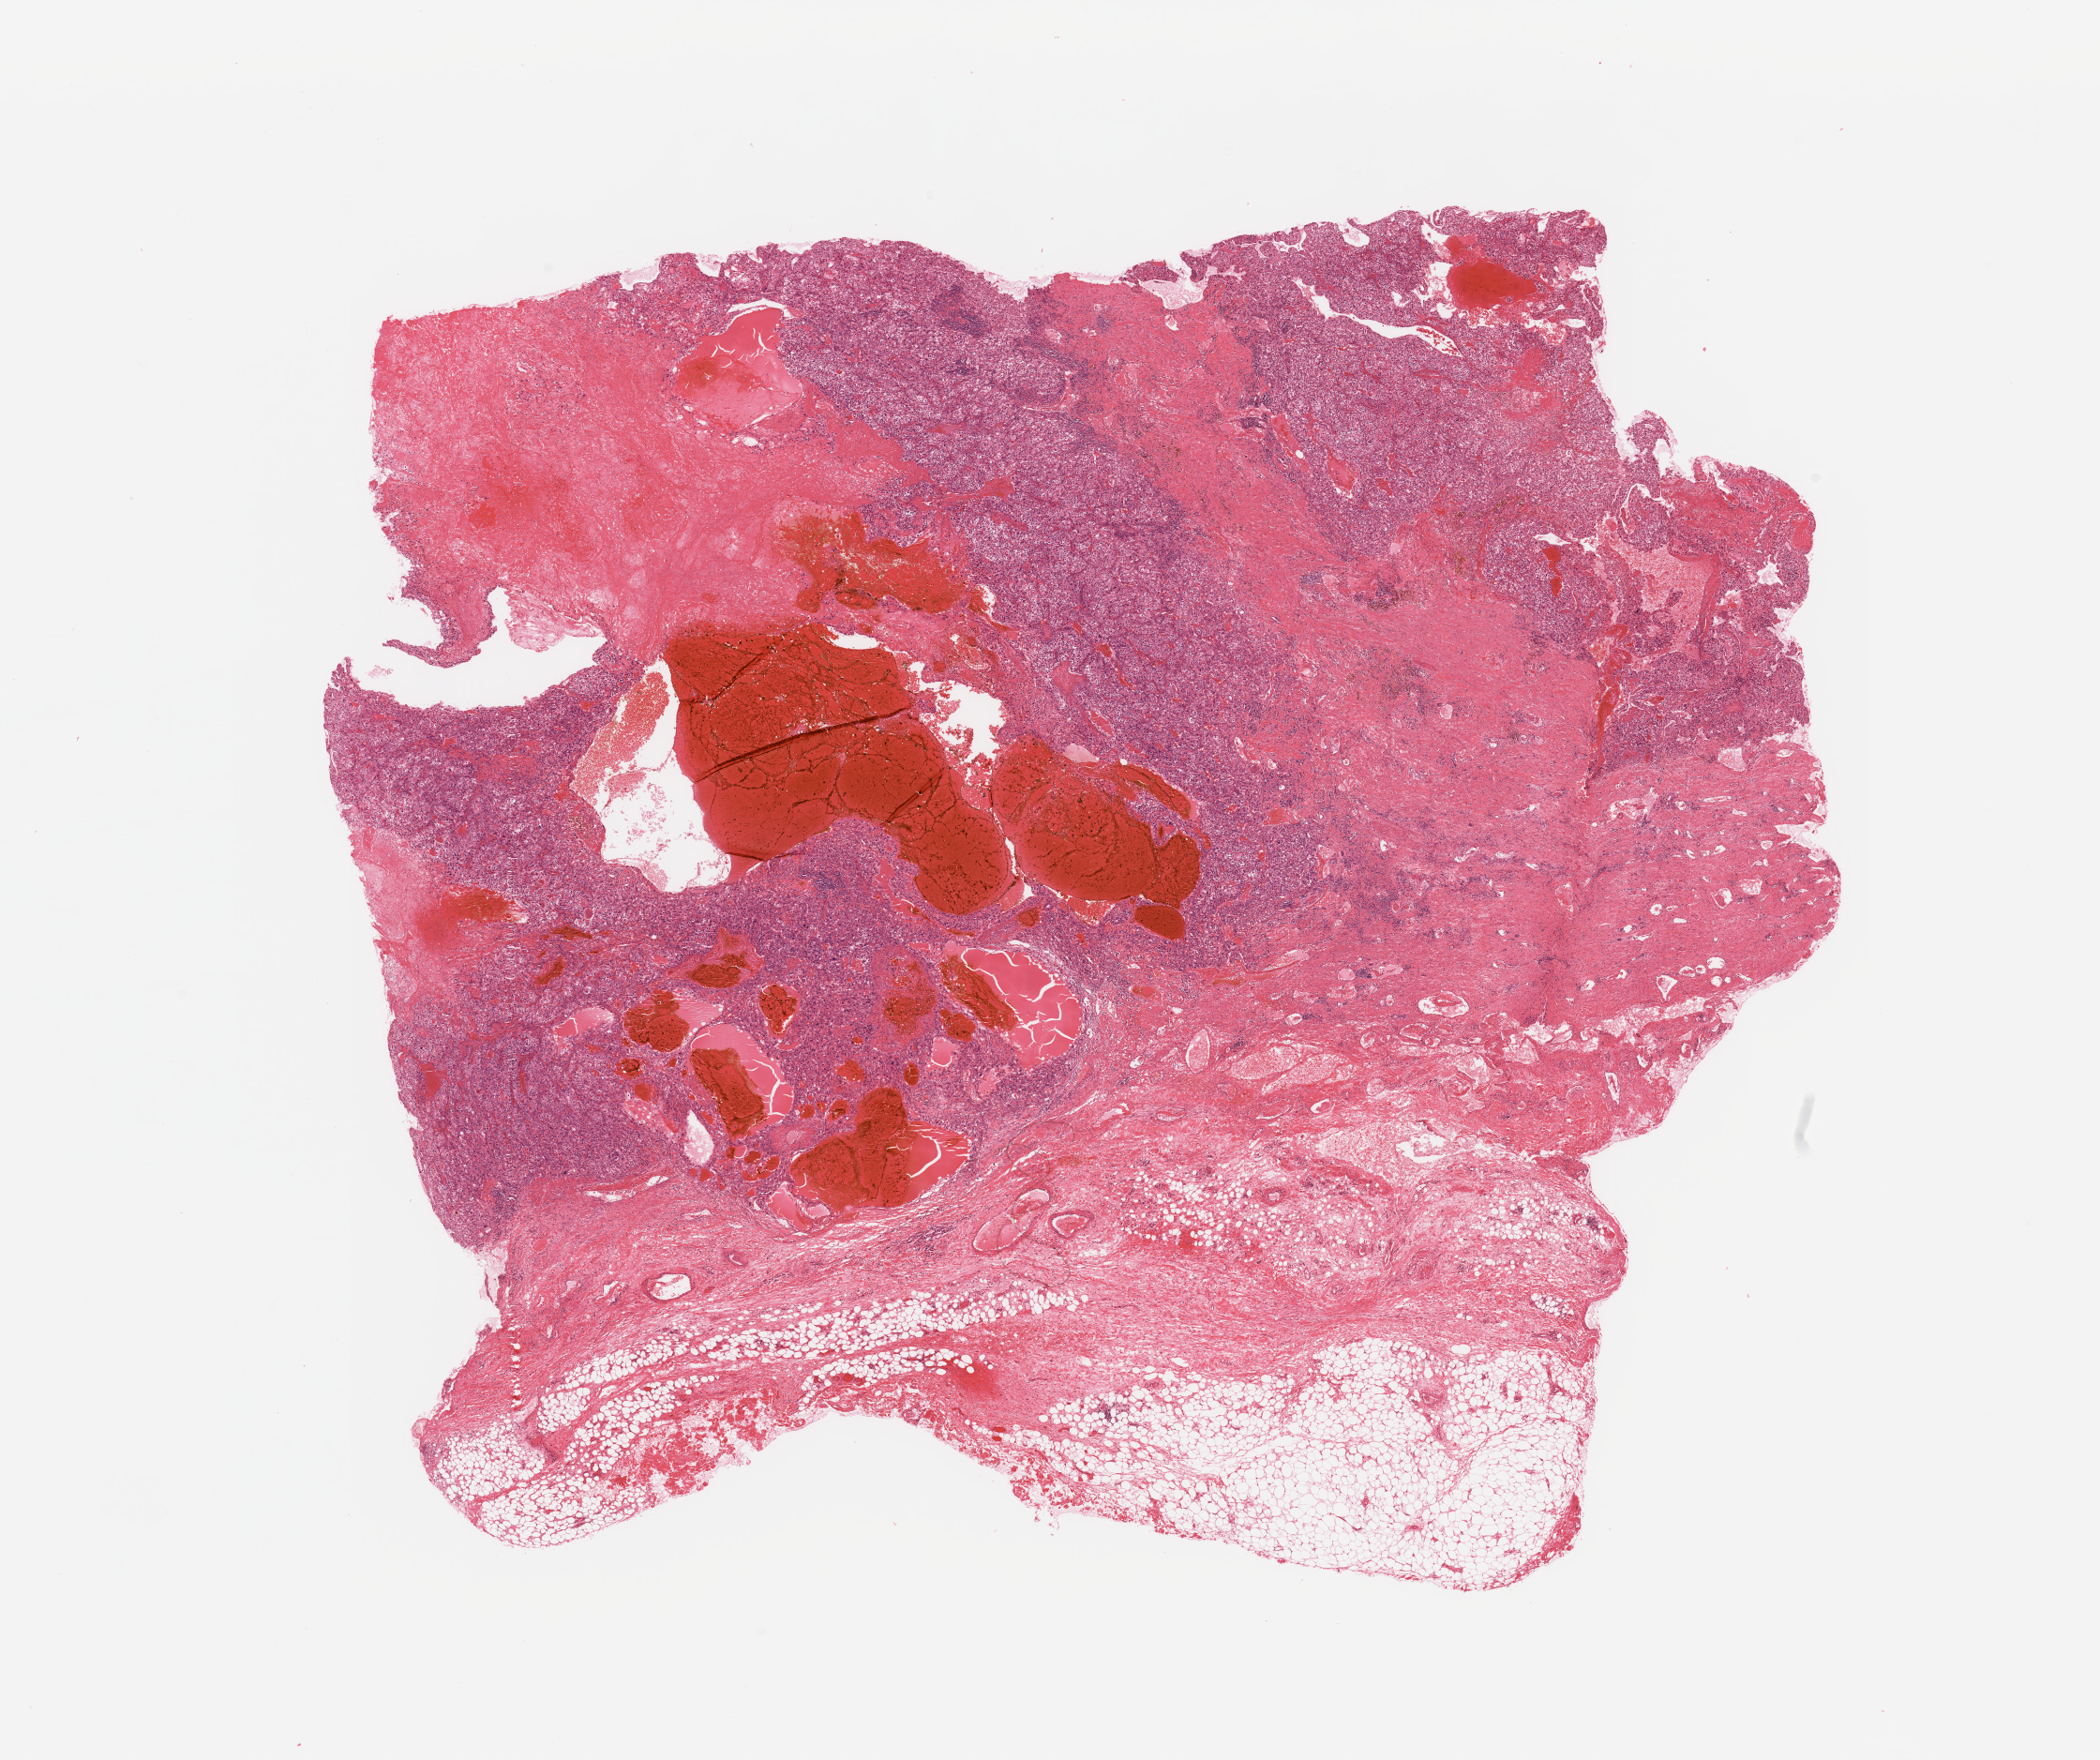
Whole-slide histology image, H&E — whole scanned area (about 17.7 x 14.8 mm, slide scanned at 20x) shown as a low-resolution overview; tumour tissue sample, sampled site: kidney. 72-year-old male patient. Histologic grade: G3 (poorly differentiated). Slide review estimates, as recorded: tumour nuclei 80%, necrosis 15%.
• histologic diagnosis: Renal cell carcinoma, NOS
• AJCC pathologic stage: IV